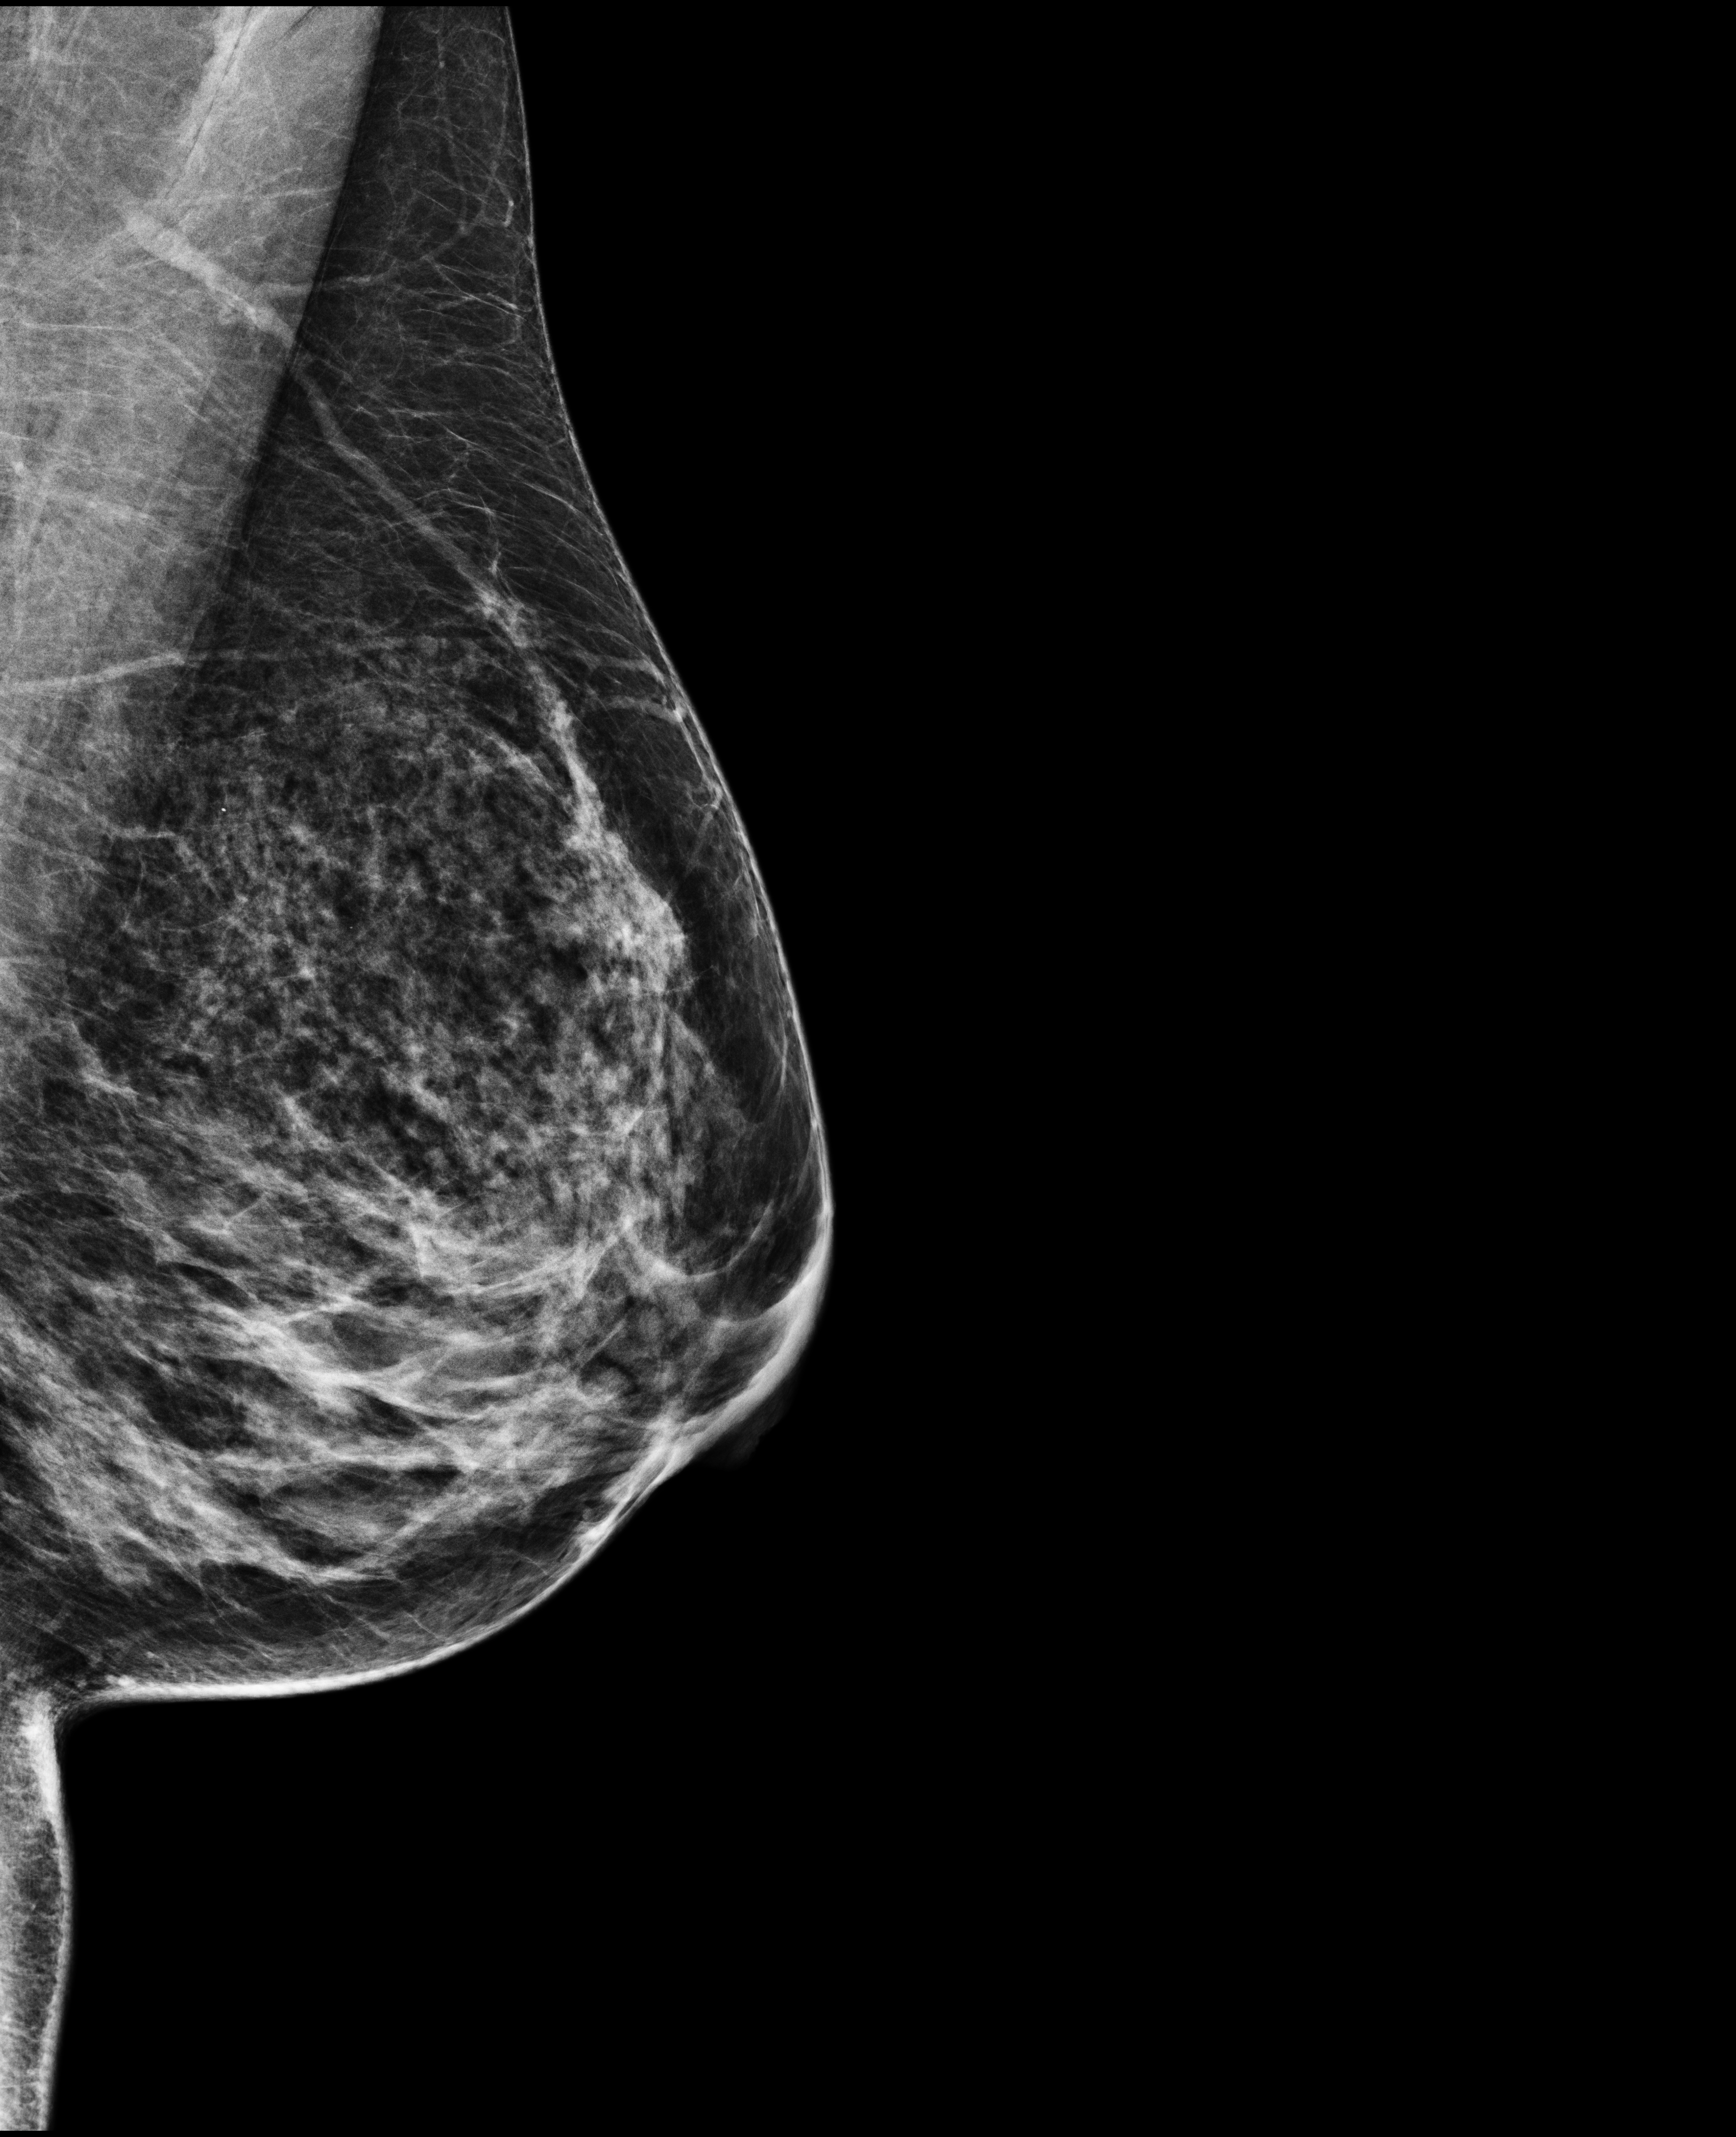
Full-field digital mammogram (FFDM); left breast; medio-lateral oblique projection; screening examination; compressed breast thickness 50 mm. Patient: female, 46 years.
- BI-RADS breast density category at the screening exam (both breasts, scale 1–4): 3
- final BI-RADS assessment for this screening round (tomosynthesis exam, both breasts): category 1
- recall: no recall after this screen